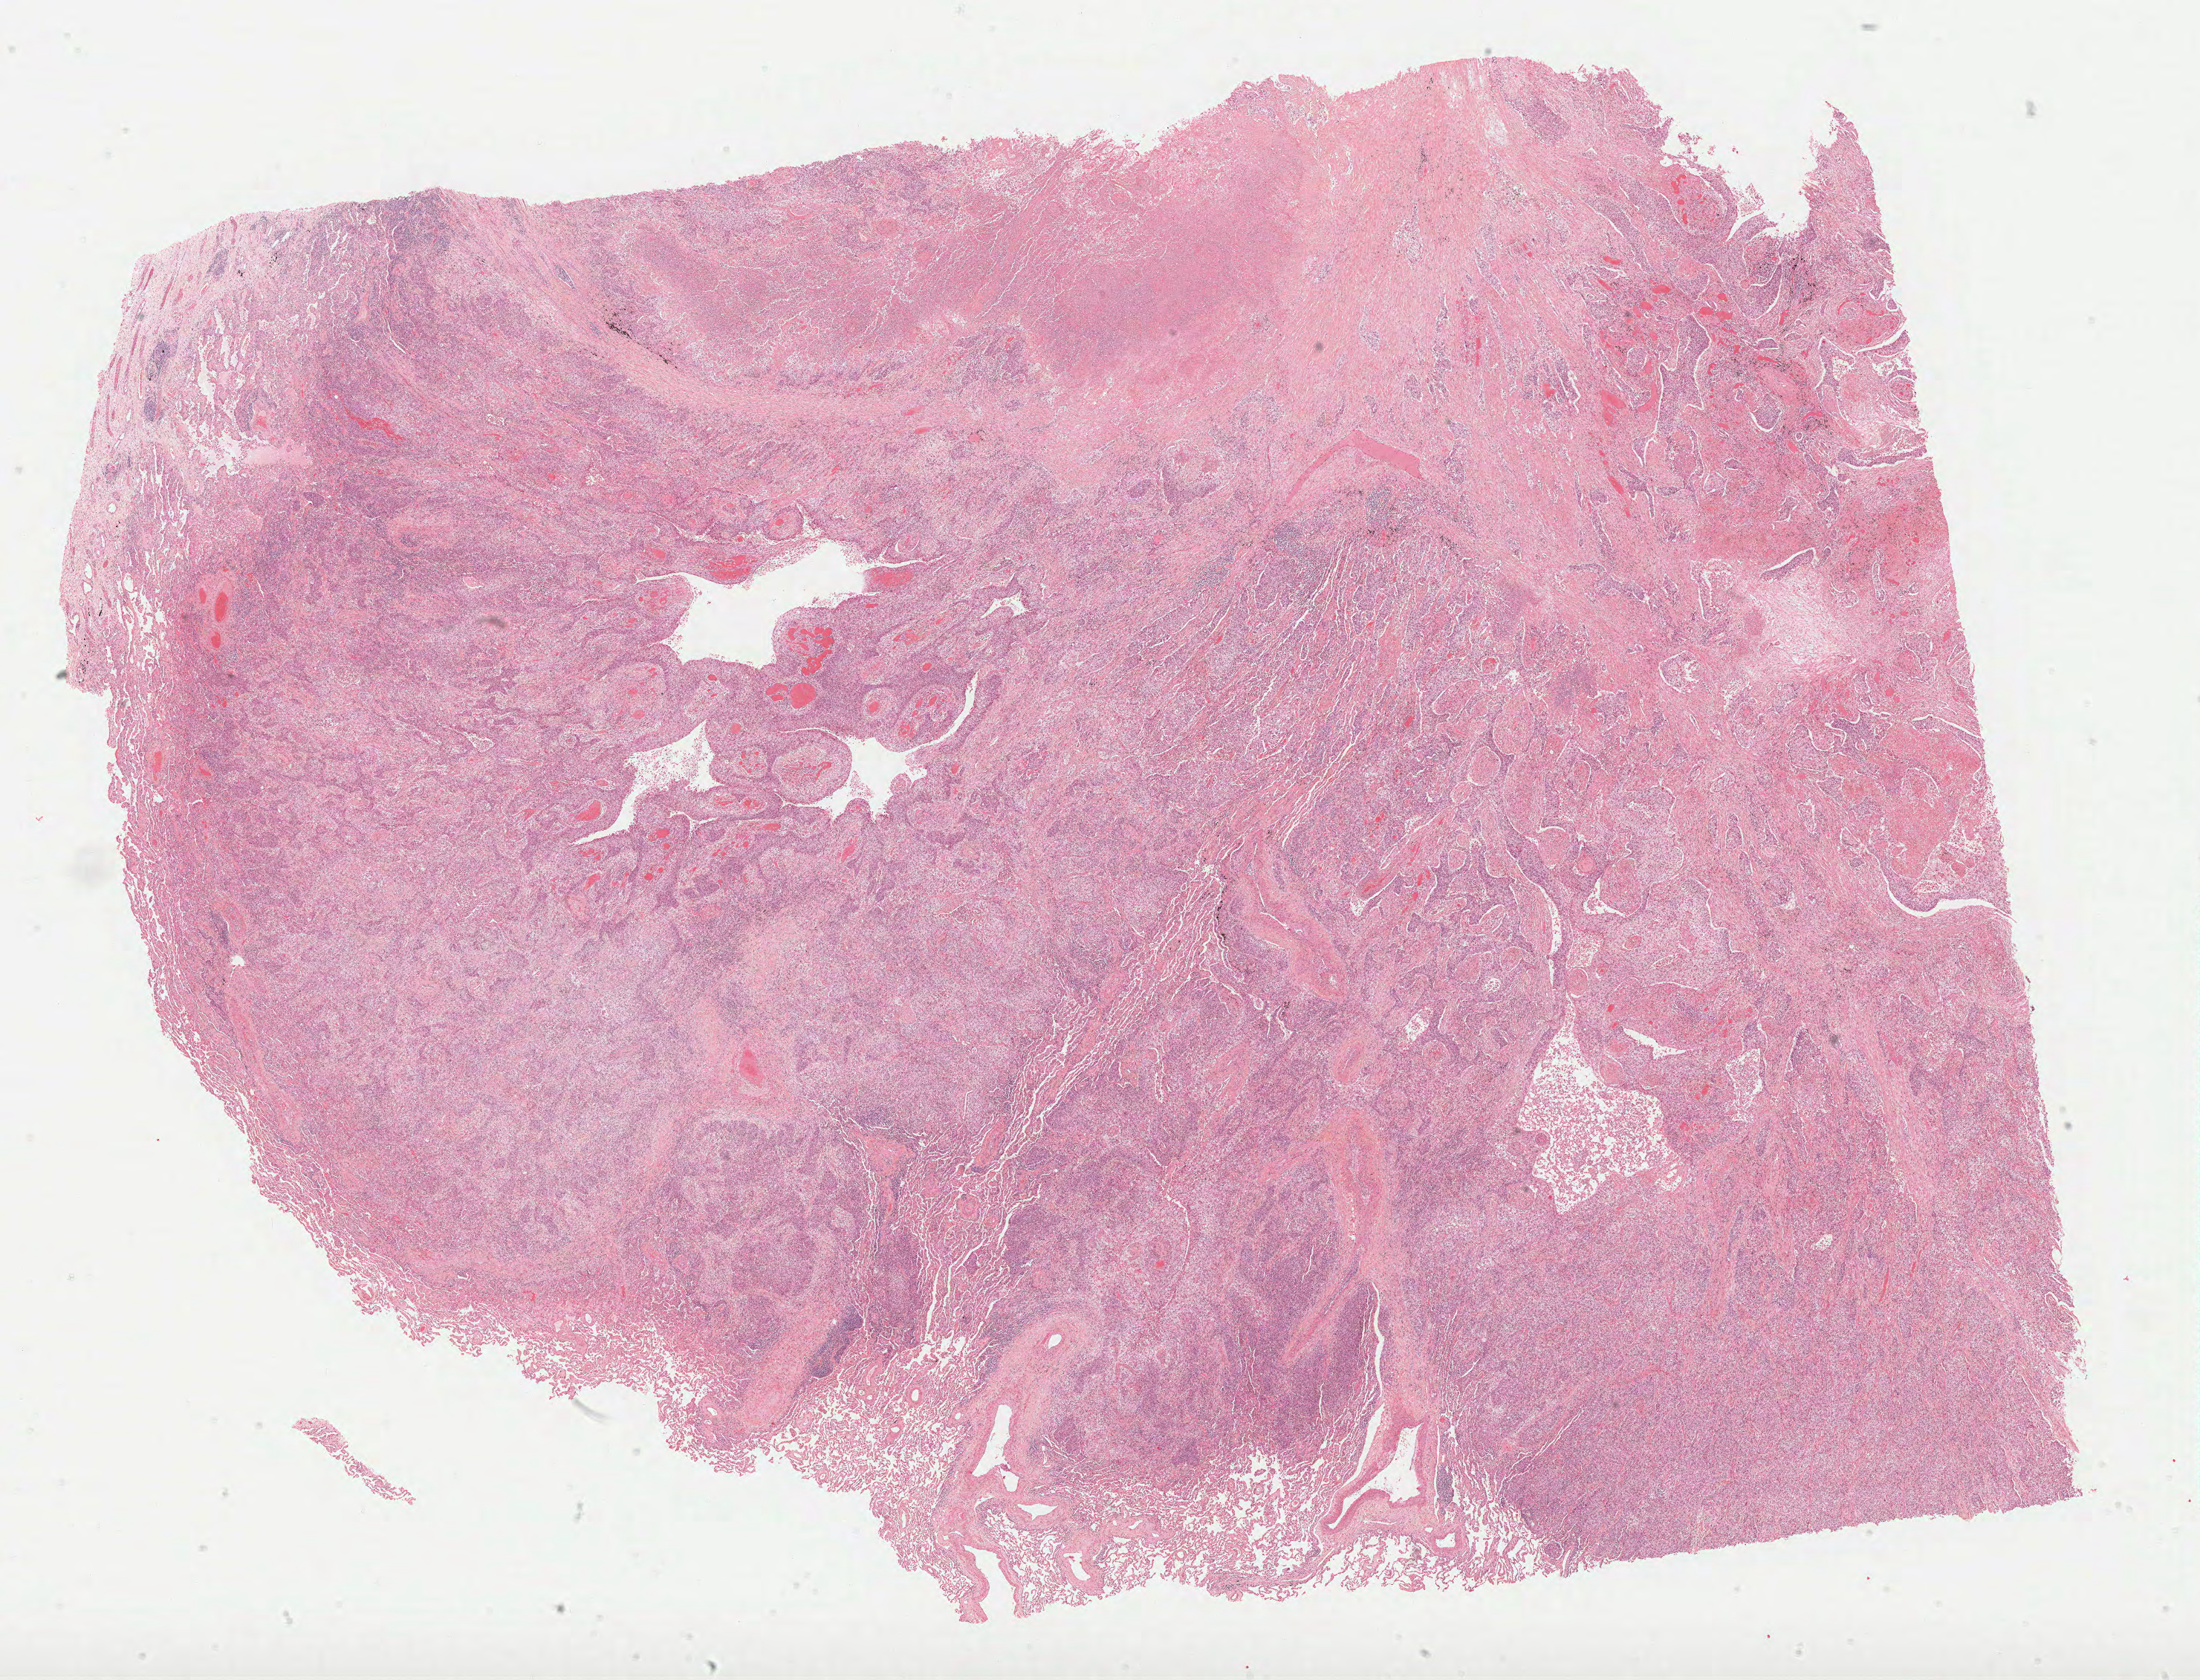
H&E whole-slide image, a low-resolution overview of the entire scanned area, about 23.9 x 18.2 mm (acquisition: 40x scan), FFPE section, sample: primary tumour, lung. Patient: male, age at initial diagnosis 65 years.
- diagnosis: Squamous cell carcinoma, NOS
- AJCC pathologic stage: IV
- laterality: right